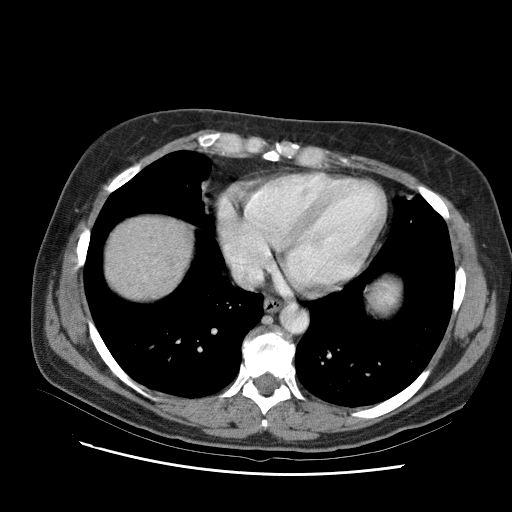
Contrast-enhanced abdominal CT (liver protocol), one axial slice; slice 89 of 95 in the series (ordered by position); reconstruction kernel STANDARD; one of 2 acquisitions stored at this slice position; soft-tissue window (W 400 / L 40 HU); 2.5 mm slice thickness; 512 × 512 image matrix, field of view 360 × 360 mm. Case-level facts recorded for this patient, not image findings: diagnosis: hepatocellular carcinoma (patient treated with transarterial chemoembolisation; whether this scan precedes or follows treatment is not stated here); TNM stage (as recorded): Stage-I; Child-Pugh class: B.
Annotated regions visible in this slice (semi-automatically segmented with operator editing):
- liver parenchyma outside the tumour (the mass and vessels are separate outlines, so this box may not span the whole liver): bounding box (x1, y1, x2, y2) in pixels: (142, 238, 152, 252)